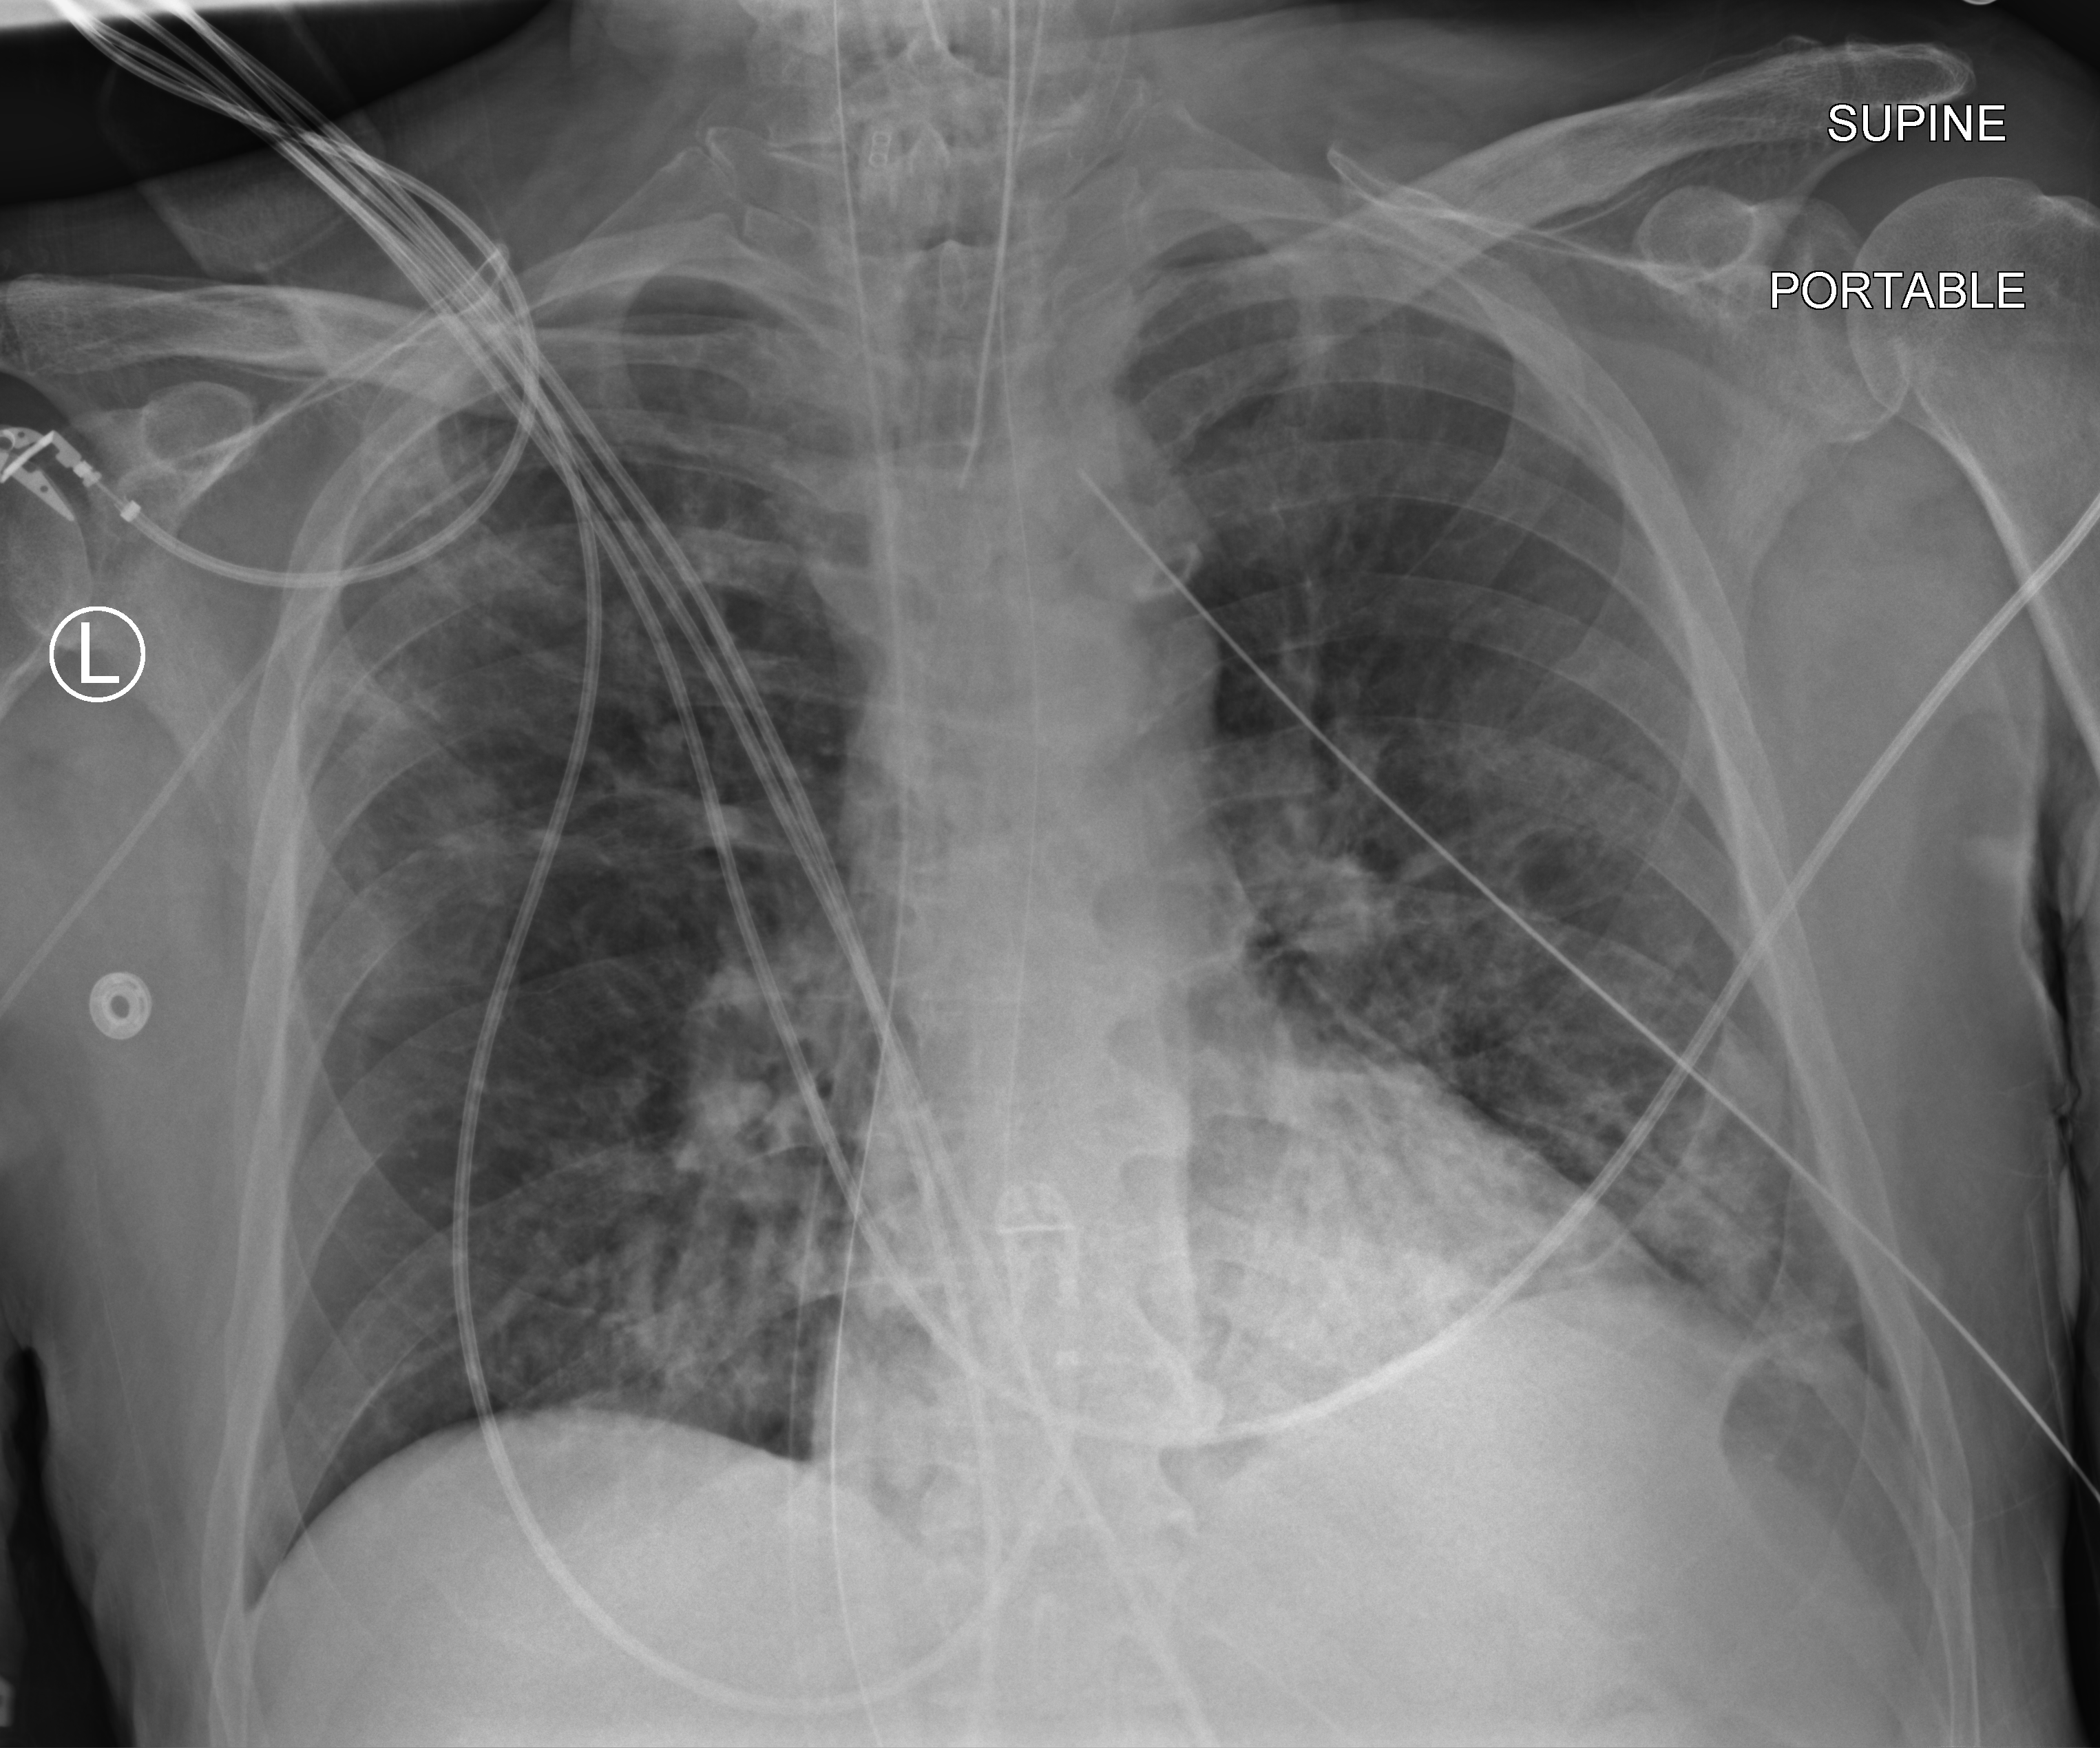
Portable chest radiograph. Male patient hospitalised with COVID-19, age 60–74 years.
From the hospital-stay record, not from the radiograph (when in the stay this image was taken is not recorded): mechanically ventilated during this hospital stay: yes; admitted to intensive care during this hospital stay: yes.